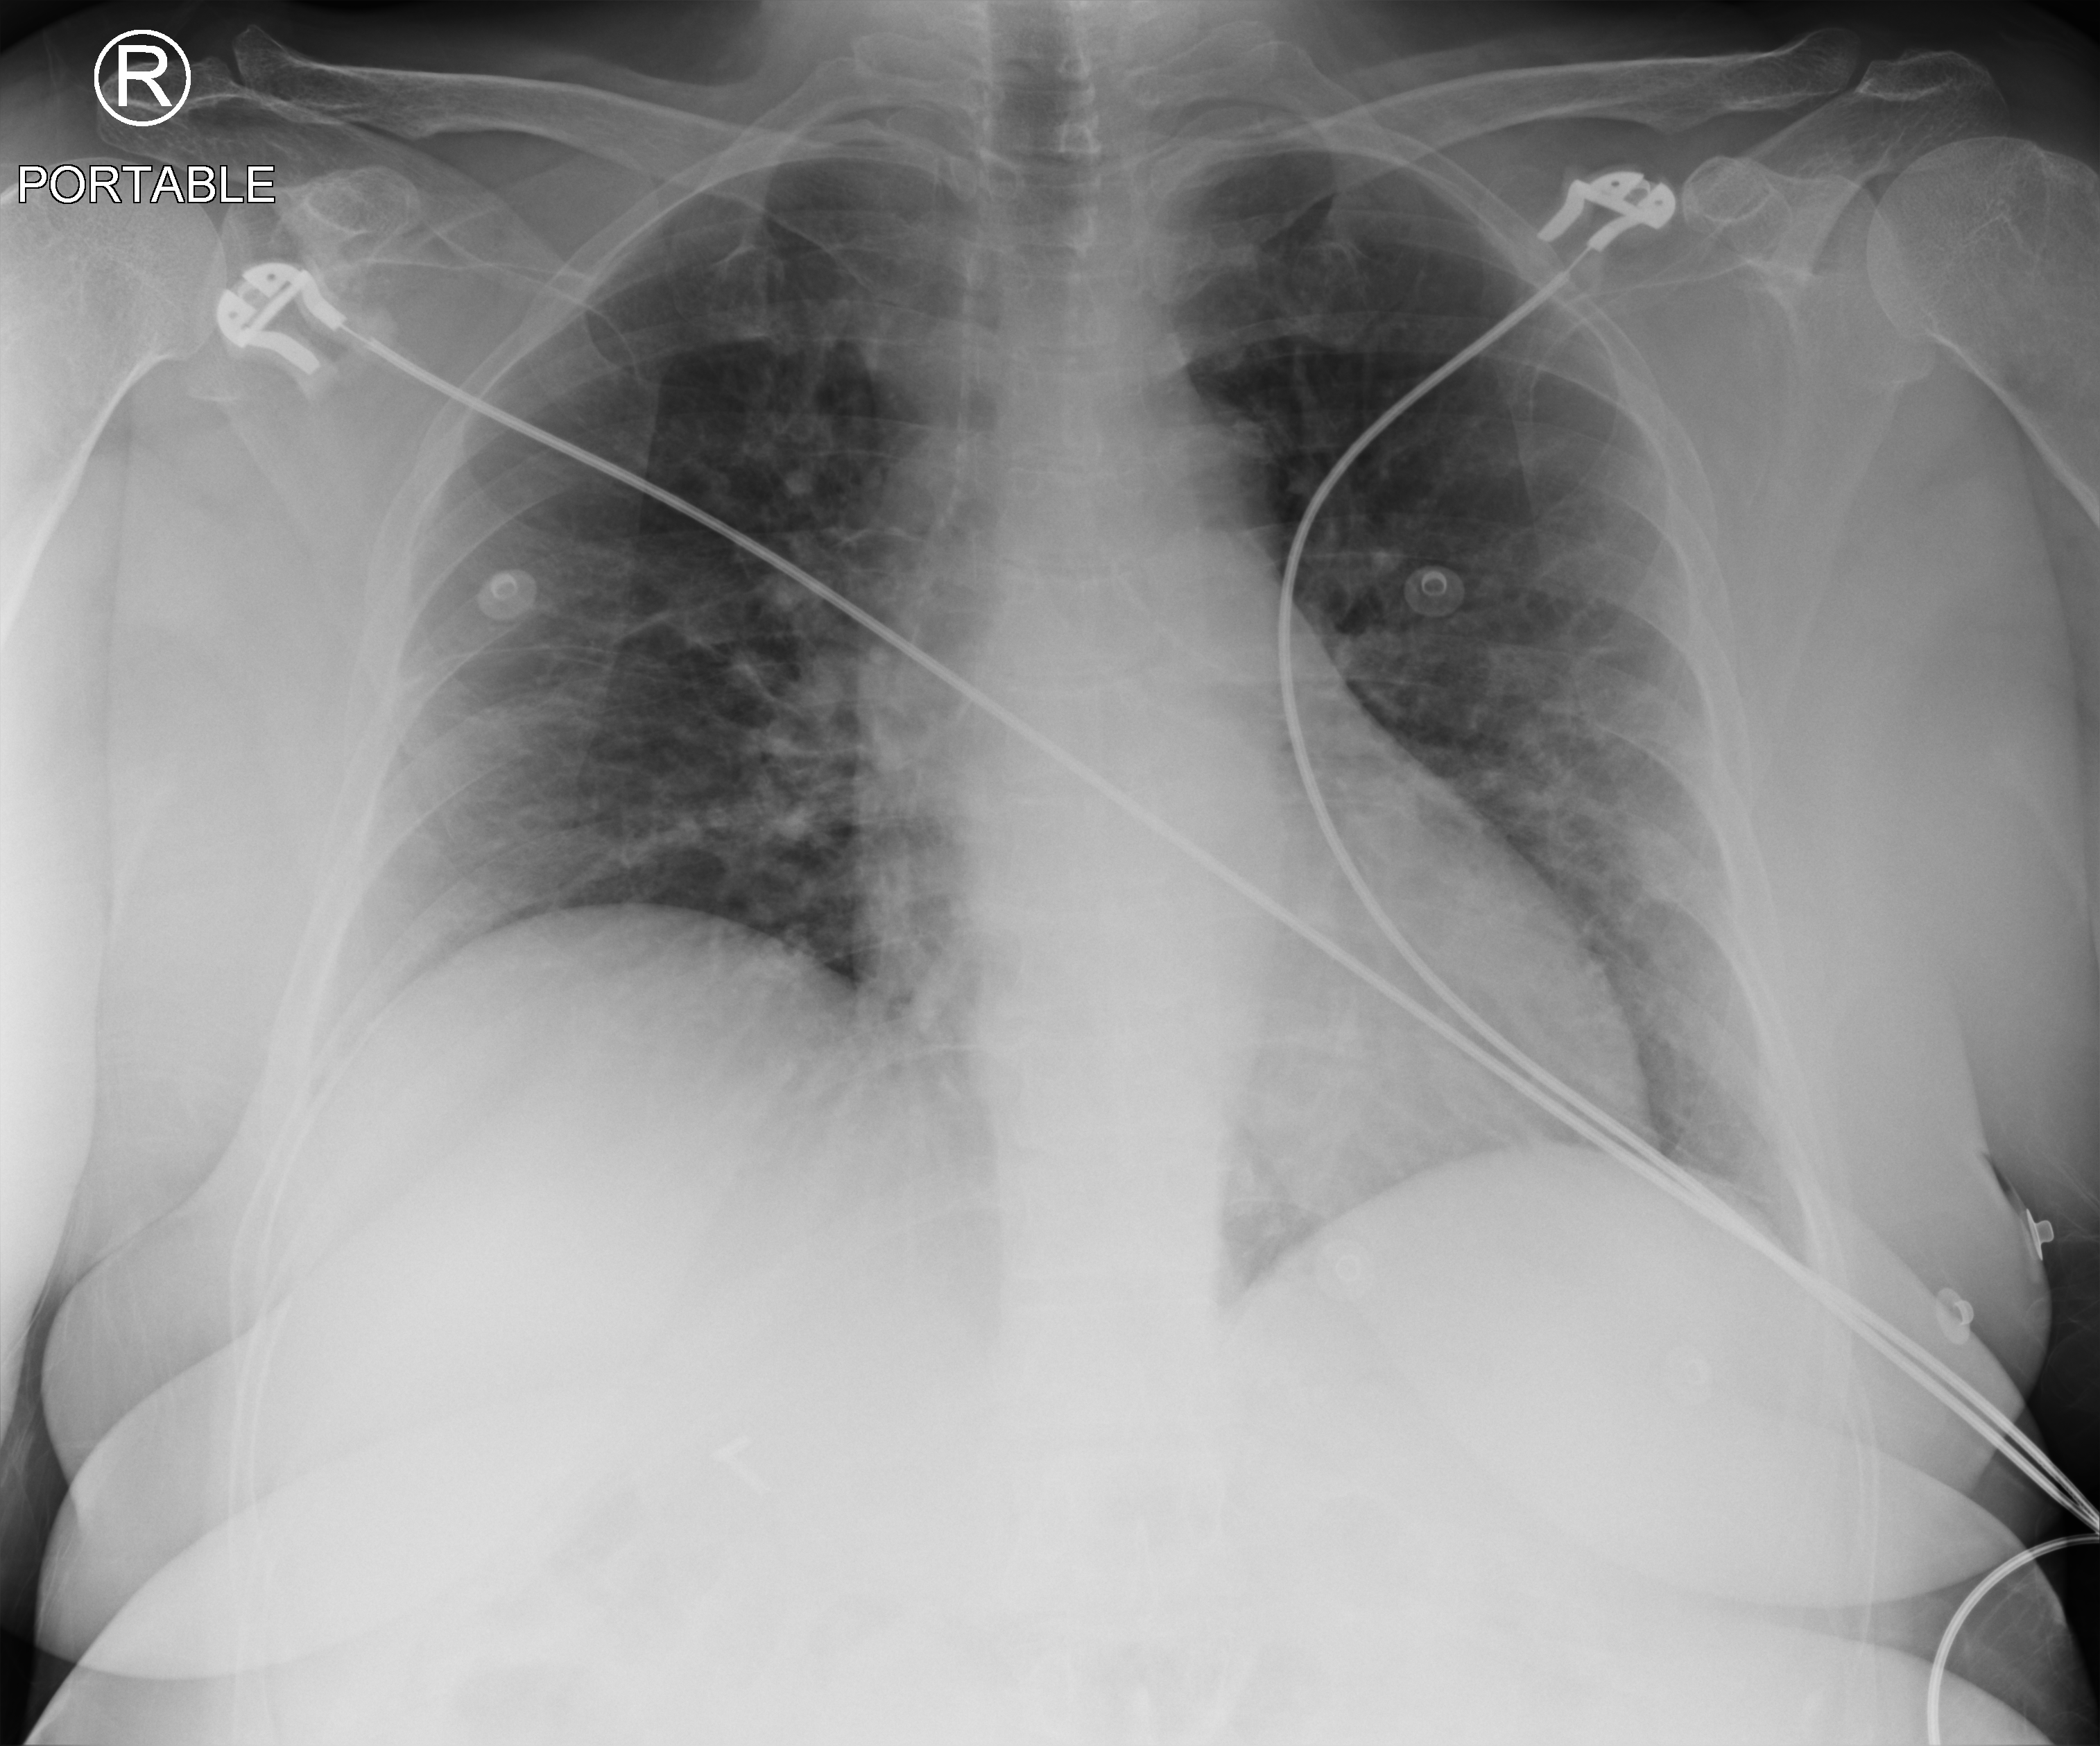
Chest X-ray (portable). Female patient hospitalised with COVID-19, age 18–59 years.
From the hospital-stay record, not from the radiograph (when in the stay this image was taken is not recorded): admitted to intensive care during this hospital stay: yes.